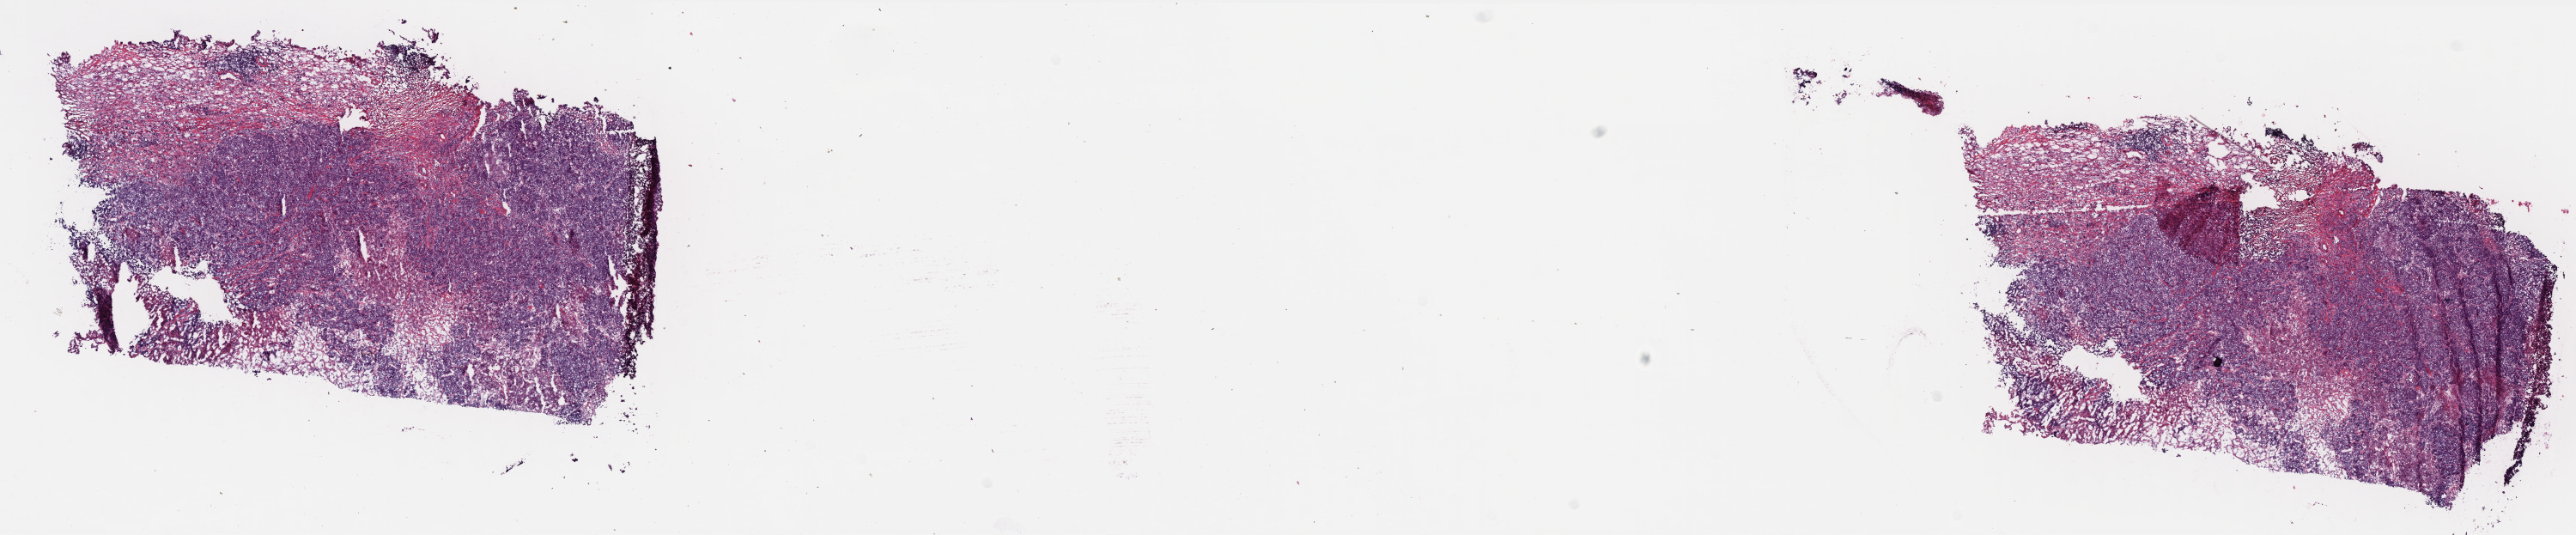
Whole-slide histology image, Hematoxylin and eosin (H&E) stained, a low-resolution overview of the entire scanned area, about 24.1 x 5.0 mm (from a 40x scan); frozen section; sample: primary tumour, breast. Female patient; age at initial diagnosis 62 years. Slide review estimates, as recorded: tumour cells 72%, tumour nuclei 70%.
Histologic diagnosis: Infiltrating duct carcinoma, NOS.